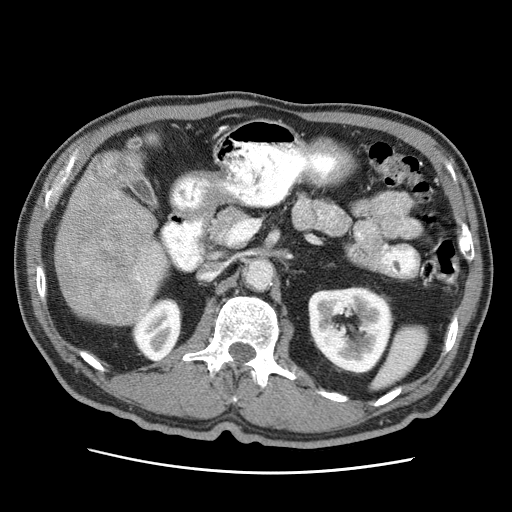
Contrast-enhanced abdominal CT (liver protocol), one axial slice. Position 15 of 75 along the scan axis. 120 kVp. Soft-tissue window (W 400 / L 40 HU). 2.5 mm slice thickness. 512 × 512 image matrix, field of view 360 × 360 mm. From the clinical record (not read from this slice): diagnosis: hepatocellular carcinoma (patient treated with transarterial chemoembolisation; whether this scan precedes or follows treatment is not stated here); TNM stage (as recorded): Stage-IIIA; Child-Pugh class: A; tumour nodularity: multinodular.
Outlined on this slice (semi-automatically segmented with operator editing):
- liver parenchyma outside the tumour (the mass and vessels are separate outlines, so this box may not span the whole liver): bounding box [x1, y1, x2, y2] px = [54, 134, 168, 326]
- mass: [56, 152, 155, 323]
- liver vessels: [138, 268, 154, 294]